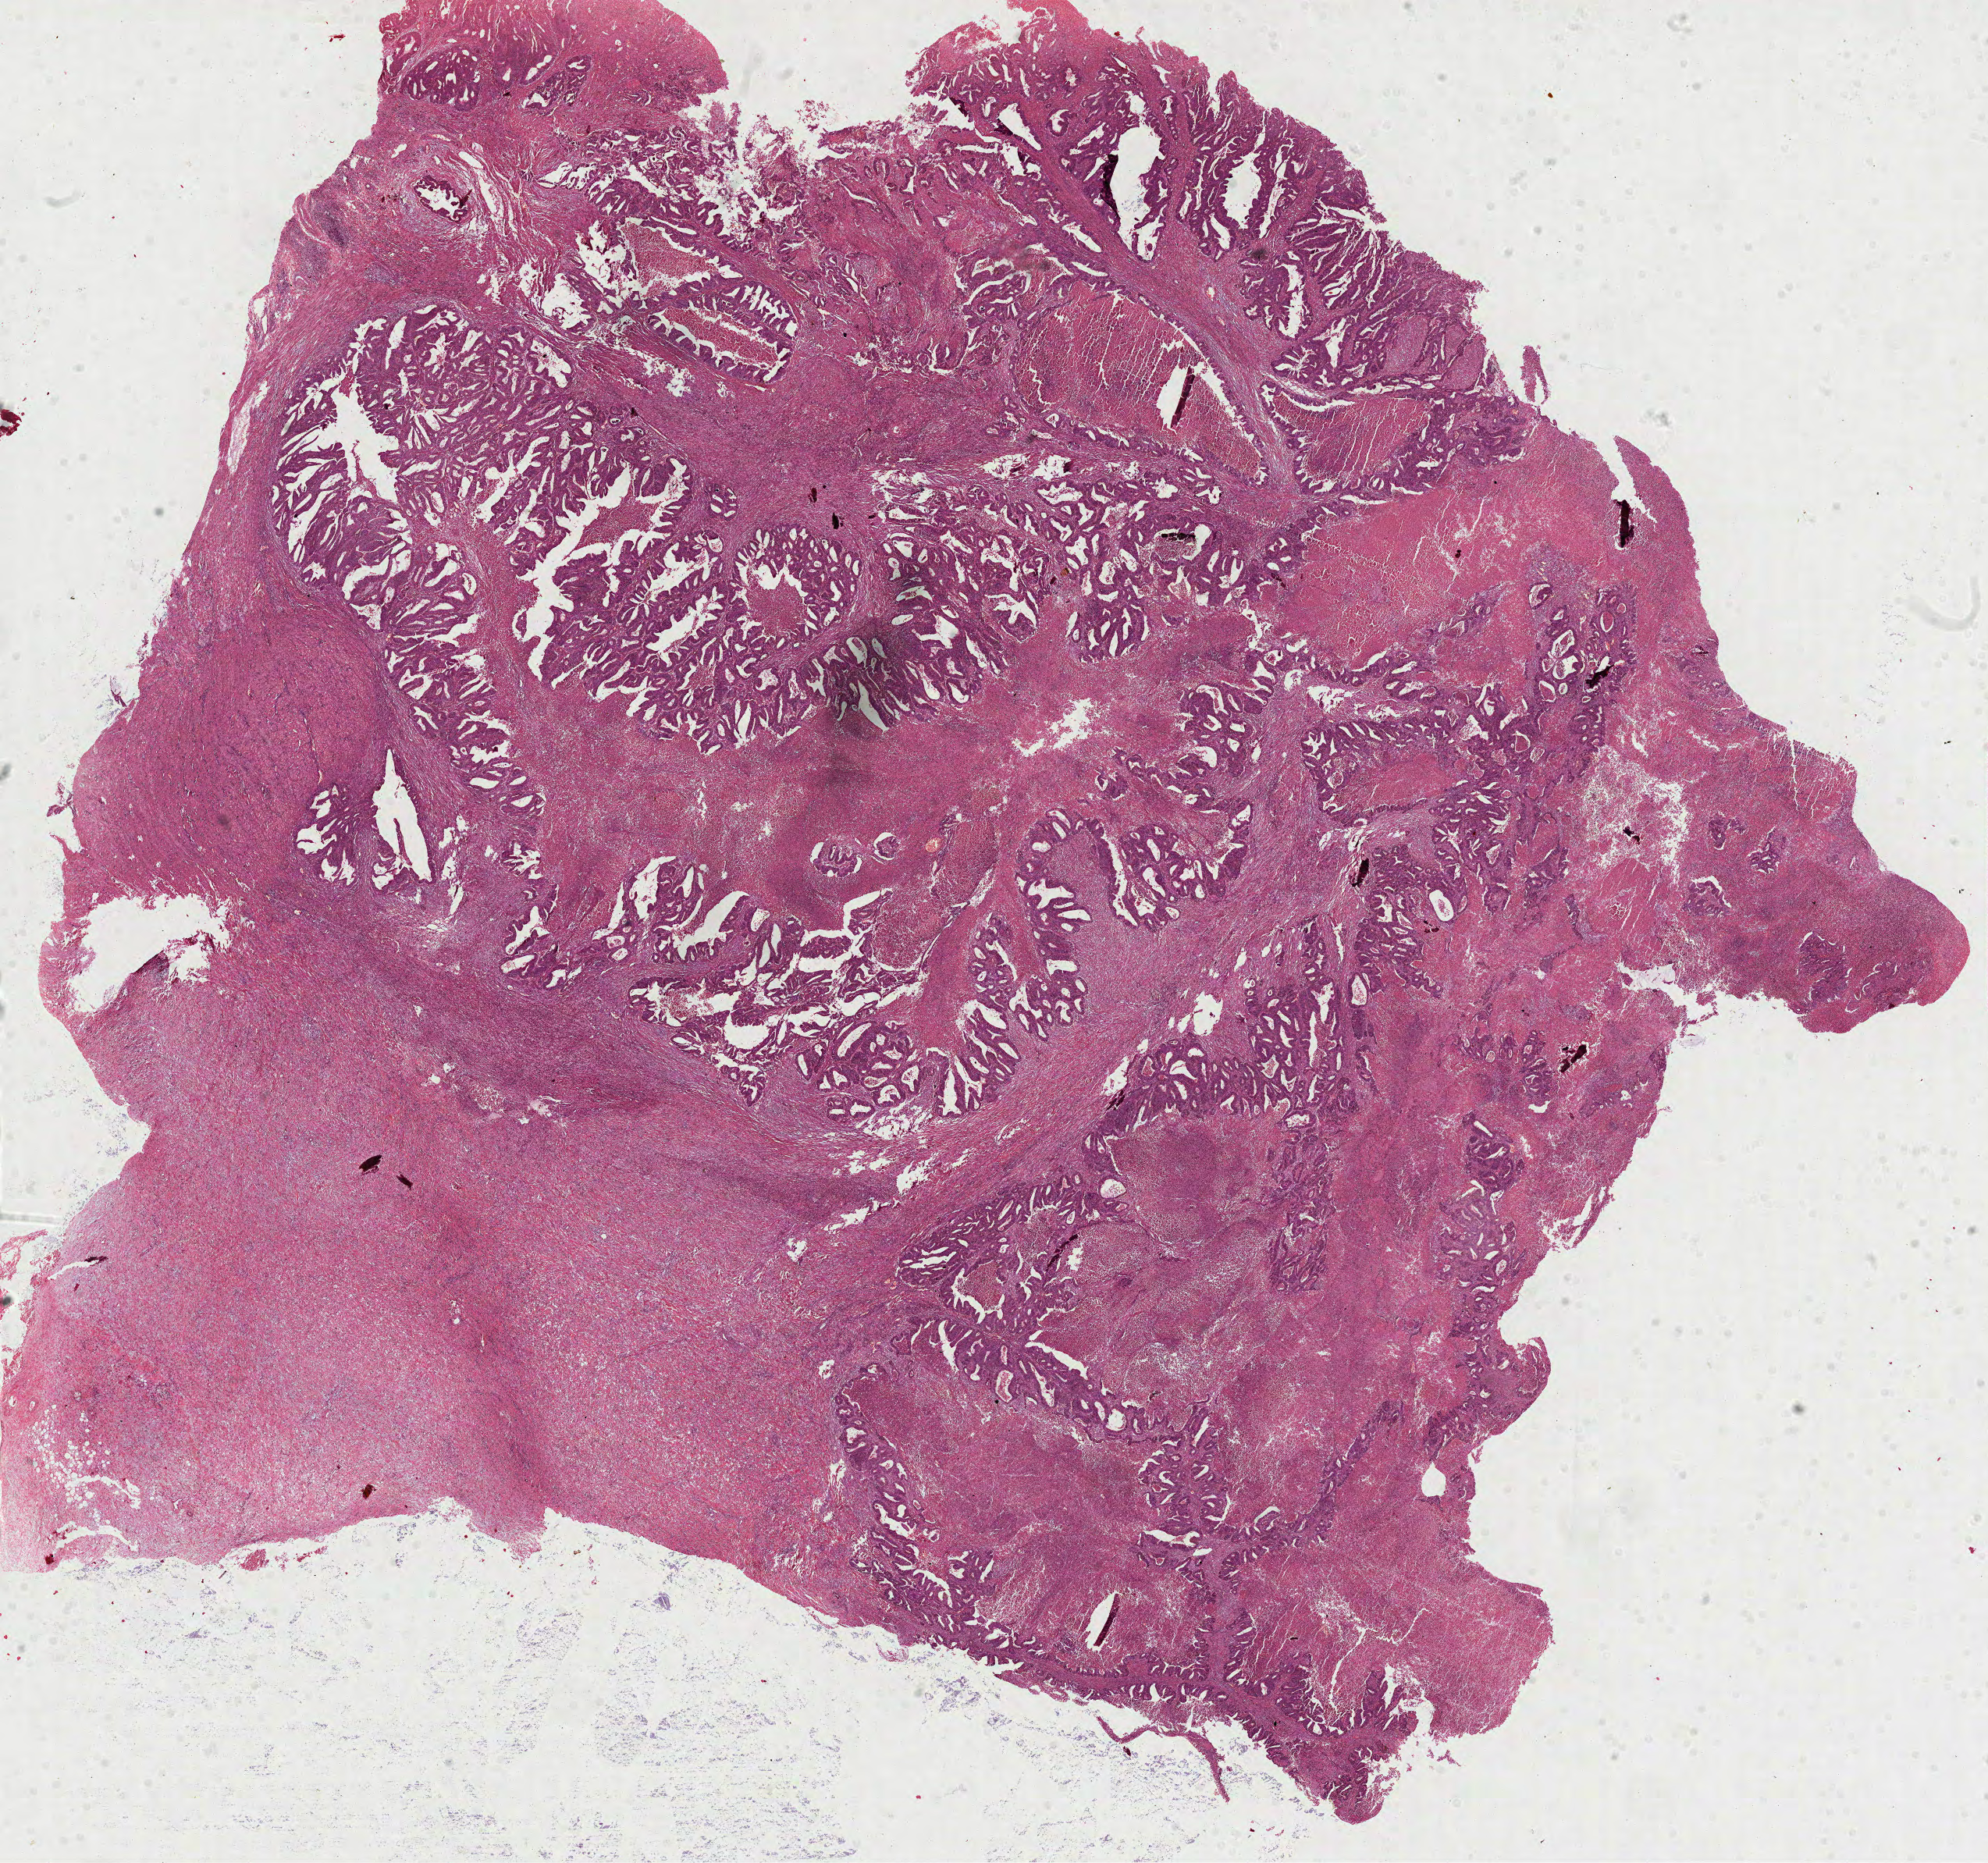
Whole-slide histology image, H&E, low-resolution overview of the scanned area, about 20.5 x 19.3 mm; formalin-fixed paraffin-embedded (FFPE) diagnostic section; primary tumour sample from the colon. Patient: male, age at initial diagnosis 63 years.
* lymph nodes positive (case pathology): 1 of 2 examined
* diagnosis: Papillary adenocarcinoma, NOS (sigmoid colon)
* AJCC pathologic stage: IIIB (6th edition)